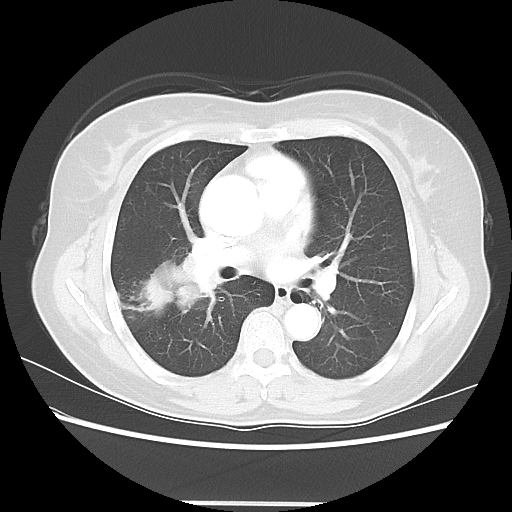
Chest CT, one axial slice; position 33 of 56 along the scan axis; reconstruction kernel LUNG; 120 kVp; lung window (W 1500 / L -600 HU); 5 mm slice thickness; 512 × 512 image matrix, field of view 360 × 360 mm. Female patient, age 55 years. From the clinical record (not read from this slice): clinical TNM (as recorded): T2 N1 M0.
Annotated regions visible in this slice (rectangle marked by the reading radiologist):
- lung tumour (recorded histology: adenocarcinoma): box from (x=128, y=250) to (x=205, y=326) px